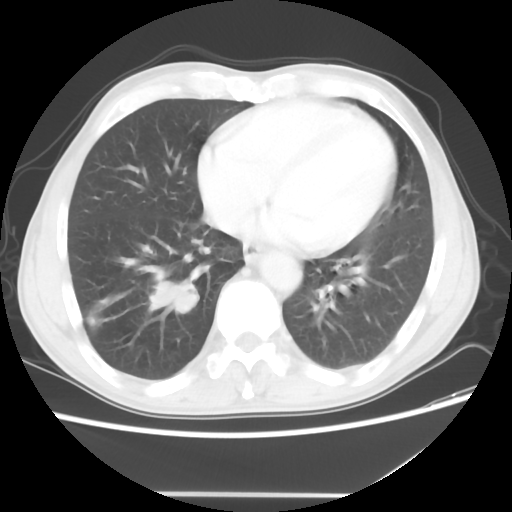
Chest CT, one axial slice; position 19 of 56 along the scan axis; 120 kVp; lung window (W 1500 / L -600 HU); 5 mm slice thickness; 512 × 512 image matrix, field of view 344 × 344 mm. Patient: male, 65 years. From the clinical record (not read from this slice): clinical TNM (as recorded): T1c N3 M0.
Structures marked on this image (bounding box drawn by a radiologist):
- lung tumour (recorded histology: small cell carcinoma): bounding box (x1, y1, x2, y2) in pixels: (142, 265, 199, 313)